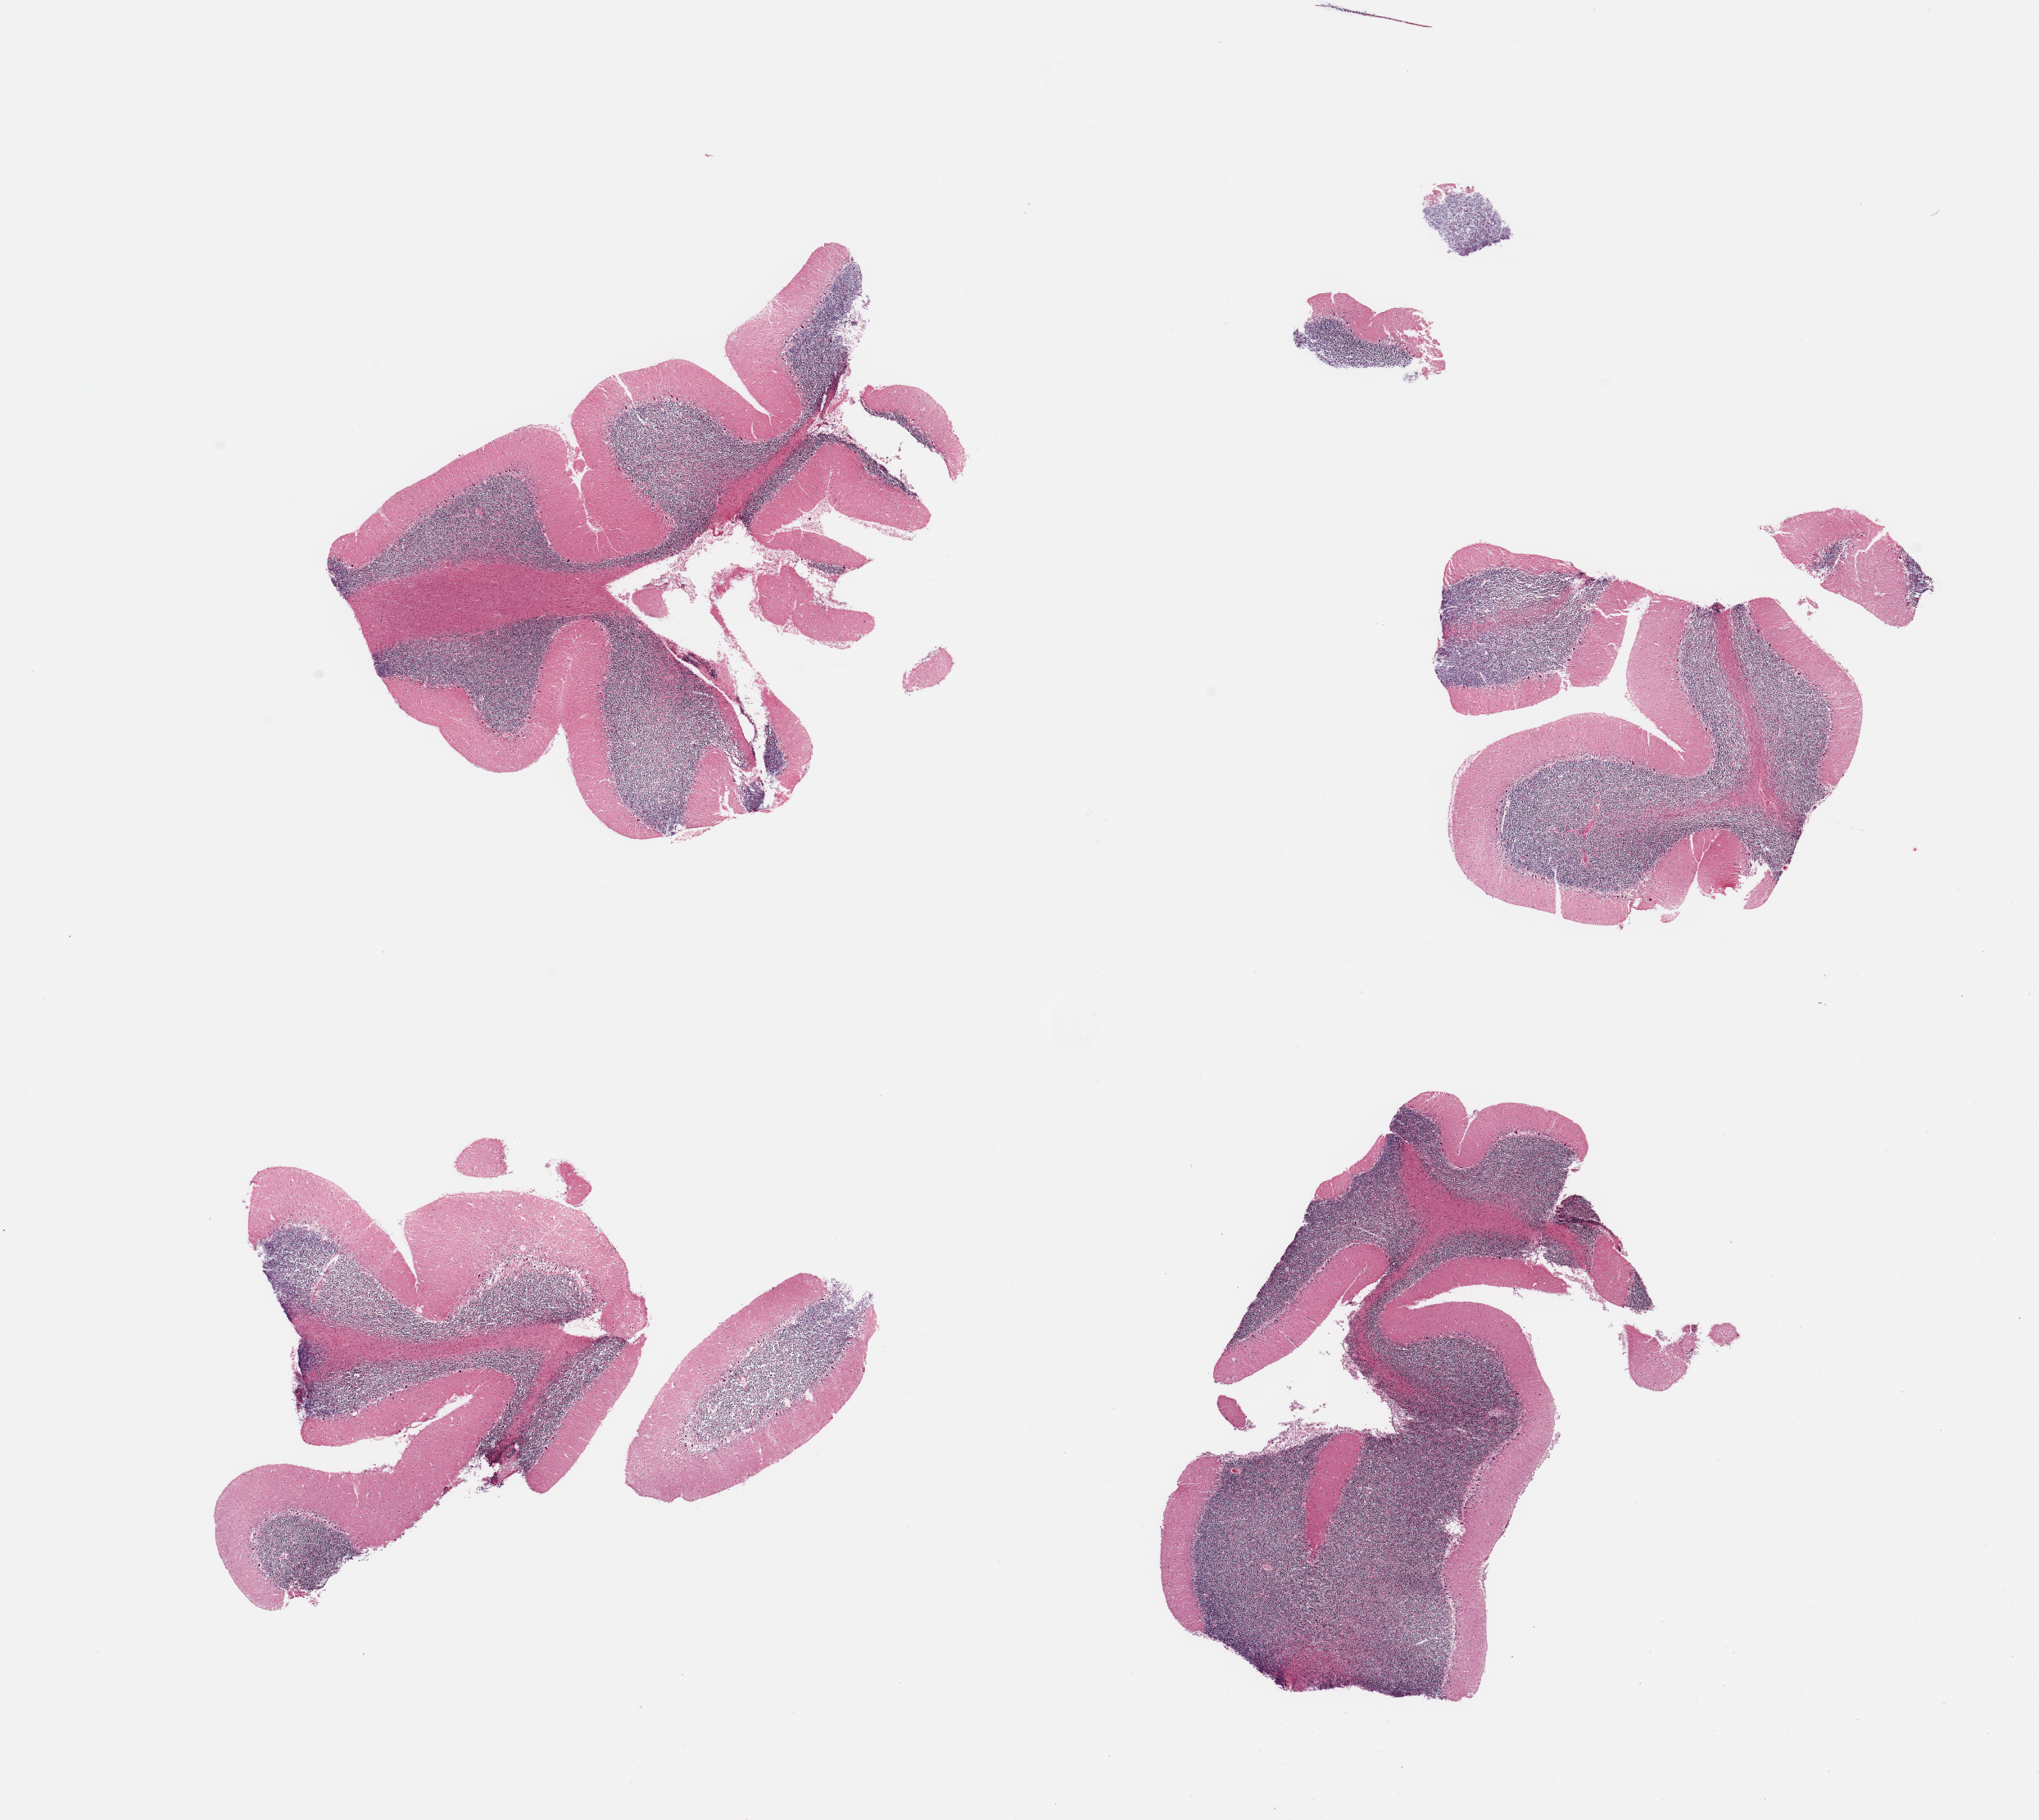
Digitized haematoxylin and eosin-stained section, shown as a low-resolution overview of the whole scanned area (about 19.7 x 17.6 mm). PAXgene-fixed paraffin-embedded (PFPE) section. Section of cerebellum (target tissue). Tissue donor sample. Male donor.
- review note (as recorded): 4 pieces; Purkinje cells well visualized, mild to moderate autolysis